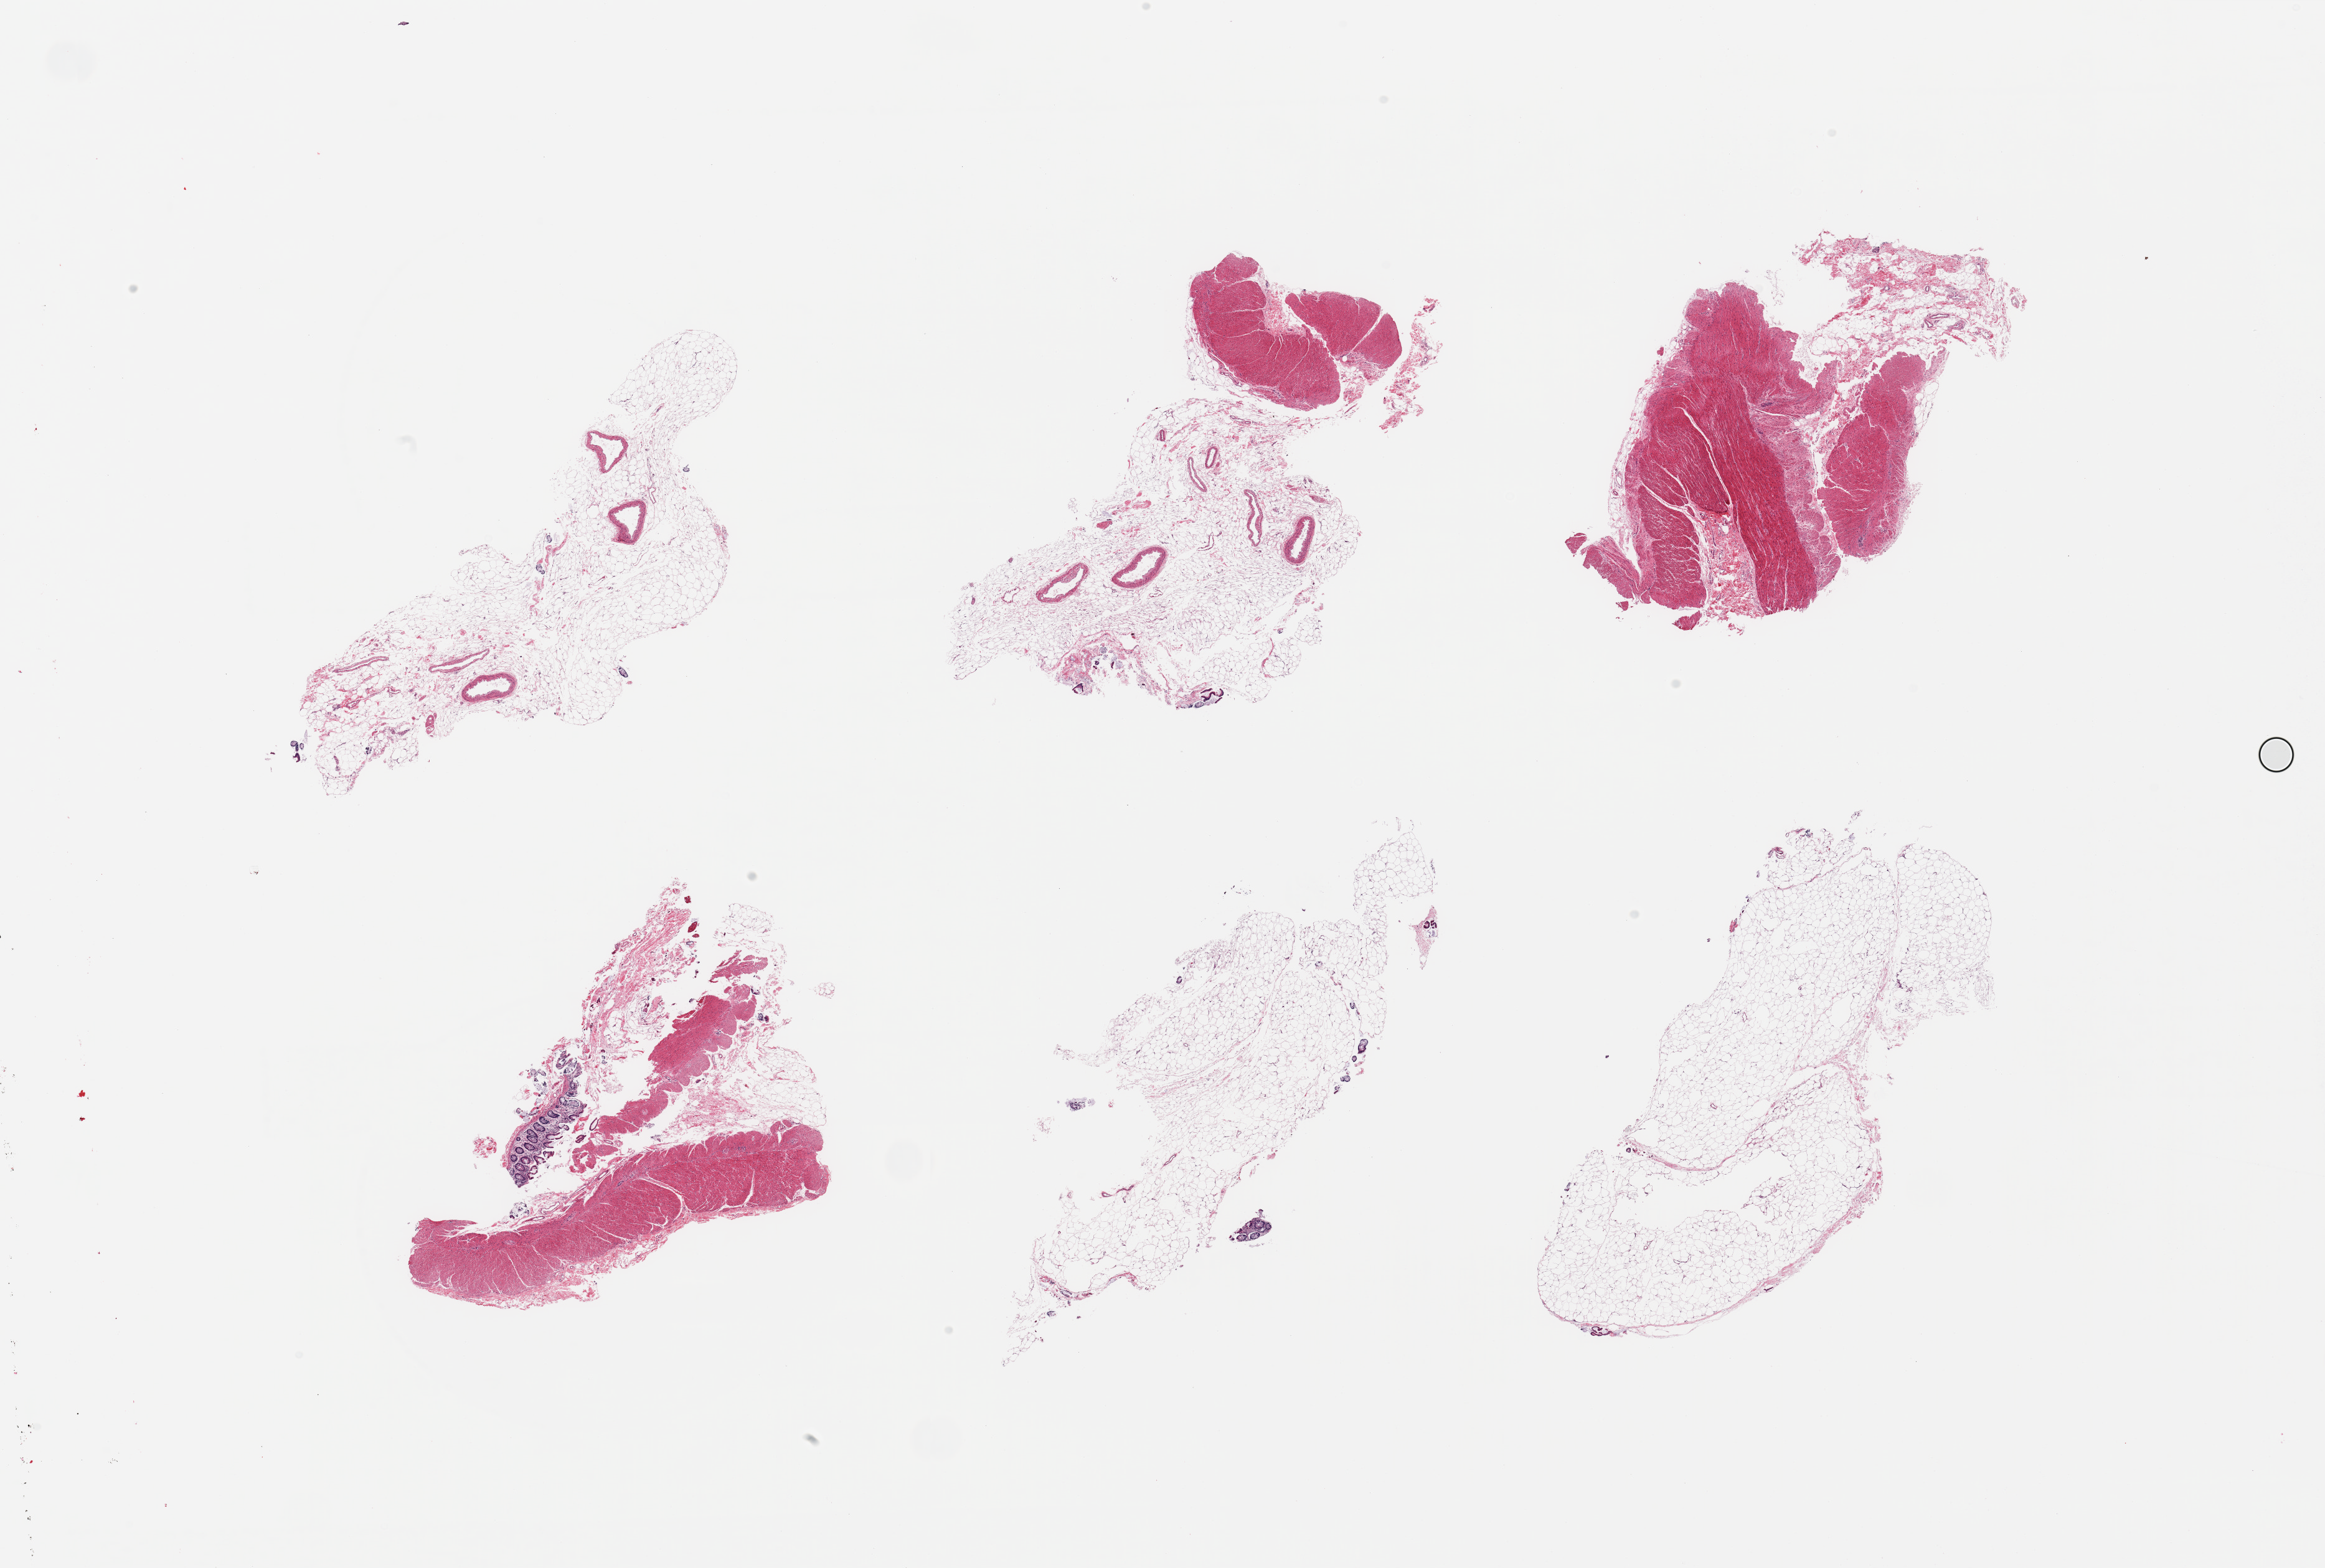
Digitized H&E-stained section, whole scanned area (about 29.5 x 19.9 mm, from a 20x scan) shown as a low-resolution overview. PAXgene-fixed paraffin-embedded (PFPE) section. Sampled site (target tissue): transverse colon. Donor tissue sample. Donor: male.
Reviewer comment on this tissue sample: 6 pieces: 3 are all fat, 1 is 80% fat; virtually no mucosa; muscle is present on 2.